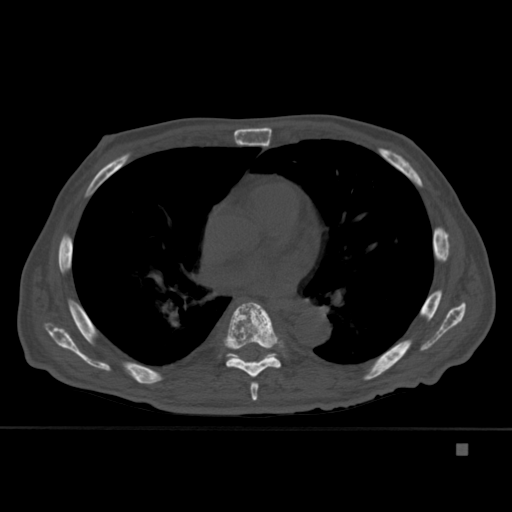
CT including the spine, one axial slice. Position 278 of 451 along the scan axis. Bone window (W 1800 / L 400 HU). 1.5 mm slice thickness. 512 × 512 image matrix, field of view 378 × 378 mm. Patient: male, 75 years. Case-level facts recorded for this patient, not image findings: primary cancer: prostate.
Outlined on this slice (semi-automatically segmented with operator editing):
- T4 vertebra: bounding box (x1, y1, x2, y2) in pixels: (272, 328, 274, 331)
- T6 vertebra: (250, 382, 259, 401)
- T7 vertebra: (224, 302, 284, 378)
- T8 vertebra: (226, 353, 276, 363)